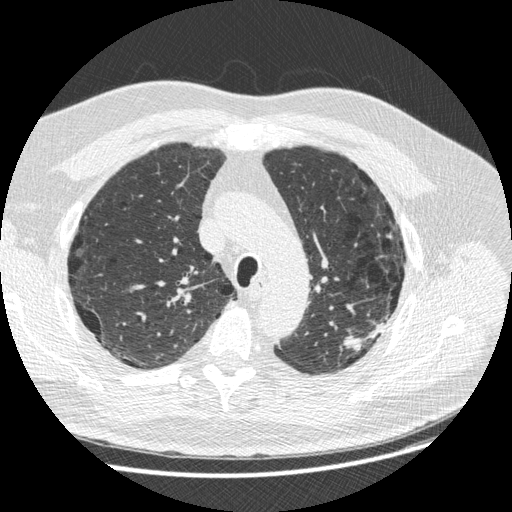
Low-dose screening chest CT, one axial slice; position 196 of 258 along the scan axis; 120 kVp; lung window (W 1500 / L -600 HU); 512 × 512 image matrix, field of view 370 × 370 mm.
Outlined on this slice (manually delineated by an expert):
- lesion 1 (tumor, upper lobe of left lung): bounding box <343,323,385,351> (left, top, right, bottom; pixels)